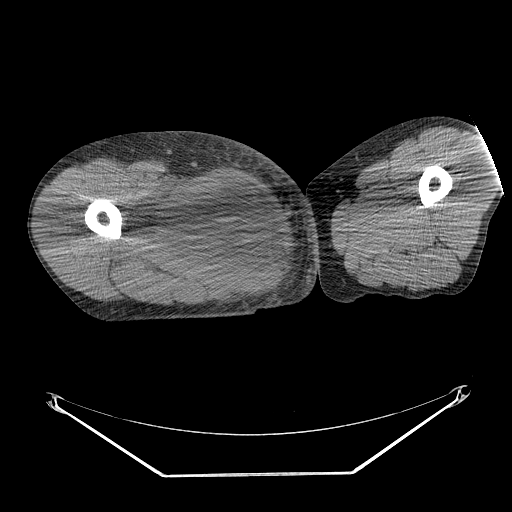
CT of an extremity soft-tissue mass (from a PET/CT study), one axial slice. Slice 248 of 311 in the series (ordered by position). Reconstruction kernel STANDARD. 140 kVp. Soft-tissue window (W 400 / L 40 HU). 512 × 512 image matrix, field of view 500 × 500 mm. Male patient. Case-level facts recorded for this patient, not image findings: histological type: undifferentiated - pleiomorphic; grade: high; site of the primary tumour: right thigh.
Outlined on this slice (expert contour drawn on MRI and transferred to this co-registered scan by the dataset authors):
- gross tumour volume including surrounding oedema: bounding box [x1, y1, x2, y2] px = [132, 174, 248, 261]
- gross tumour volume (mass): [155, 176, 248, 261]